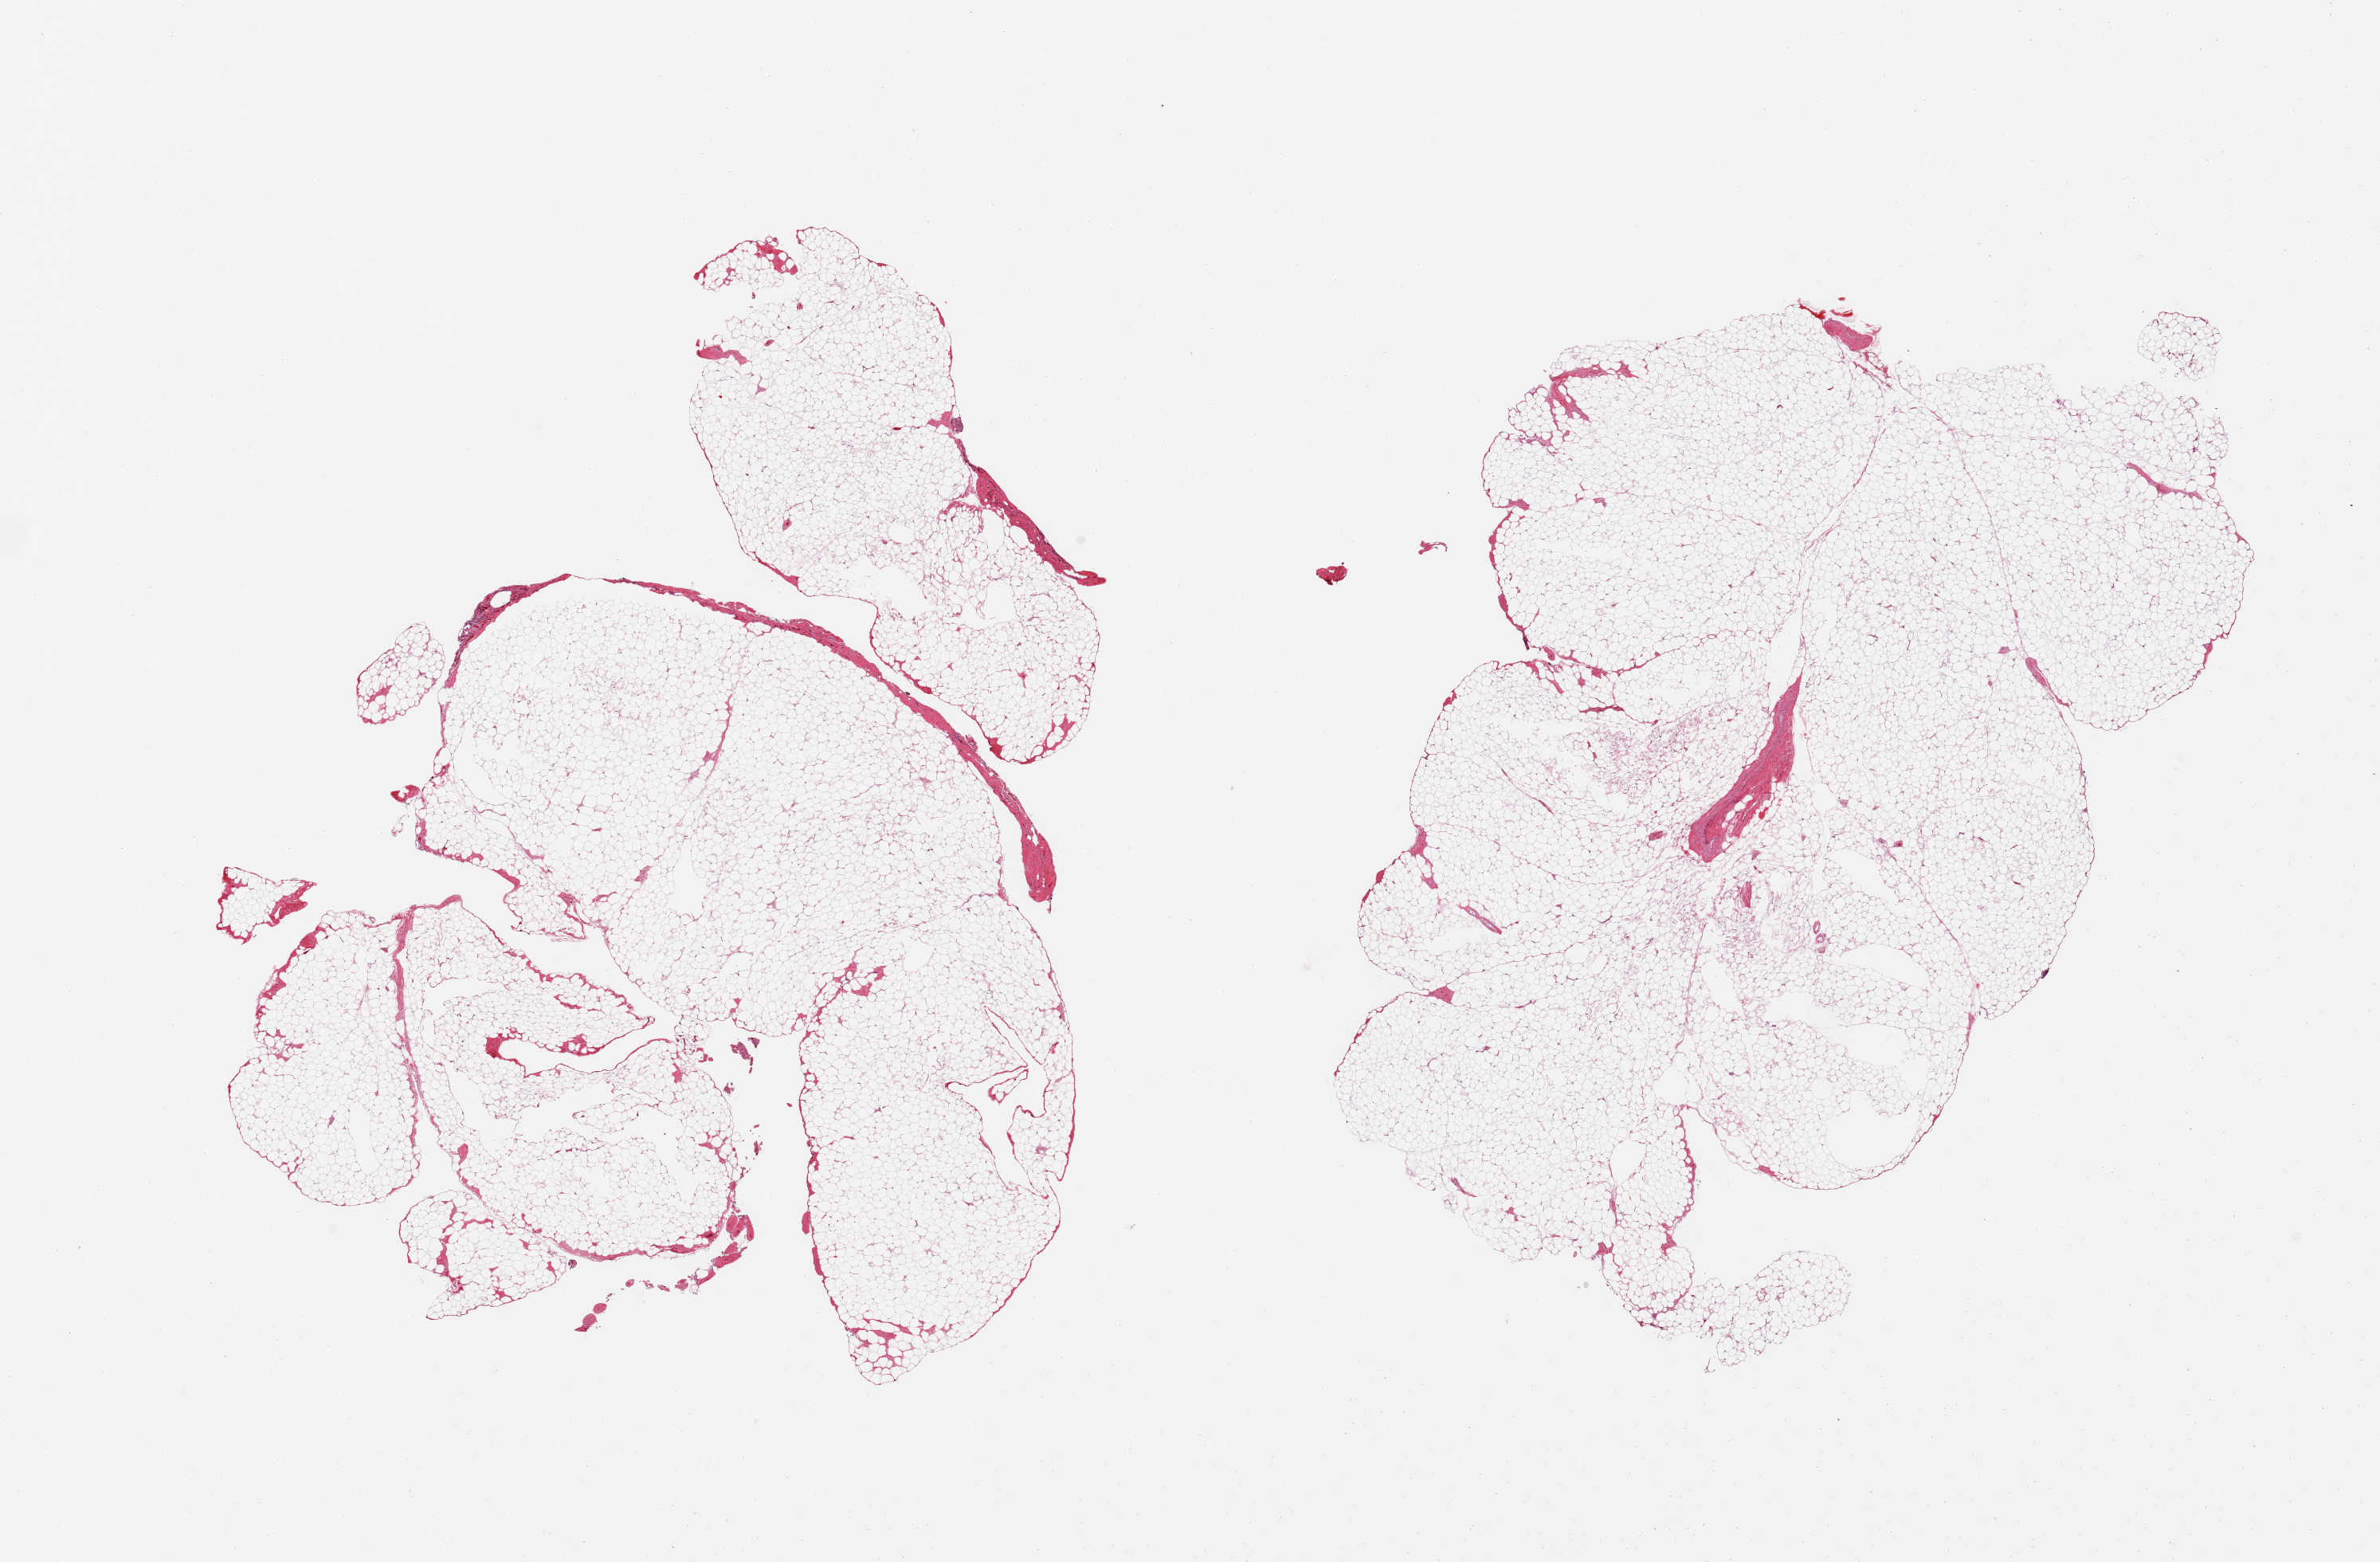
Haematoxylin and eosin whole-slide image — low-resolution overview of the scanned area, about 23.6 x 15.5 mm (from a 20x scan). PAXgene-fixed, paraffin-embedded tissue. Sampled site (target tissue): omentum. Tissue donor sample. Donor: female.
- reviewer comment on this tissue sample: 2 pieces, fascia is ~5% of tissue